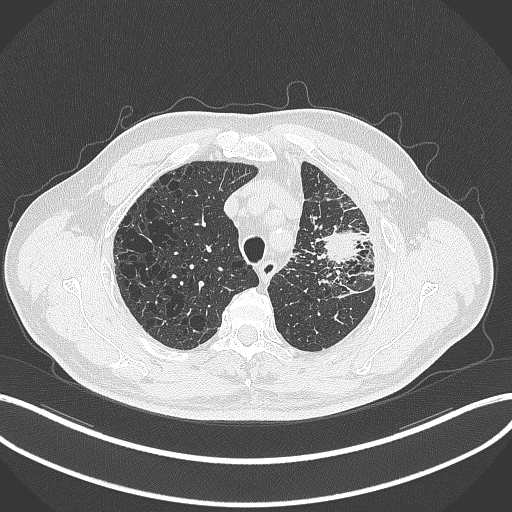
Chest CT, one axial slice; slice 256 of 297 in the series (ordered by position); reconstruction kernel B70f; lung window (W 1500 / L -600 HU); 512 × 512 image matrix, field of view 400 × 400 mm. Patient: male, 68 years. From the clinical record (not read from this slice): clinical TNM (as recorded): T3 N3 M1.
Outlined on this slice (bounding box drawn by a radiologist):
- lung tumour (recorded histology: adenocarcinoma): bounding box [x1, y1, x2, y2] px = [318, 225, 367, 265]